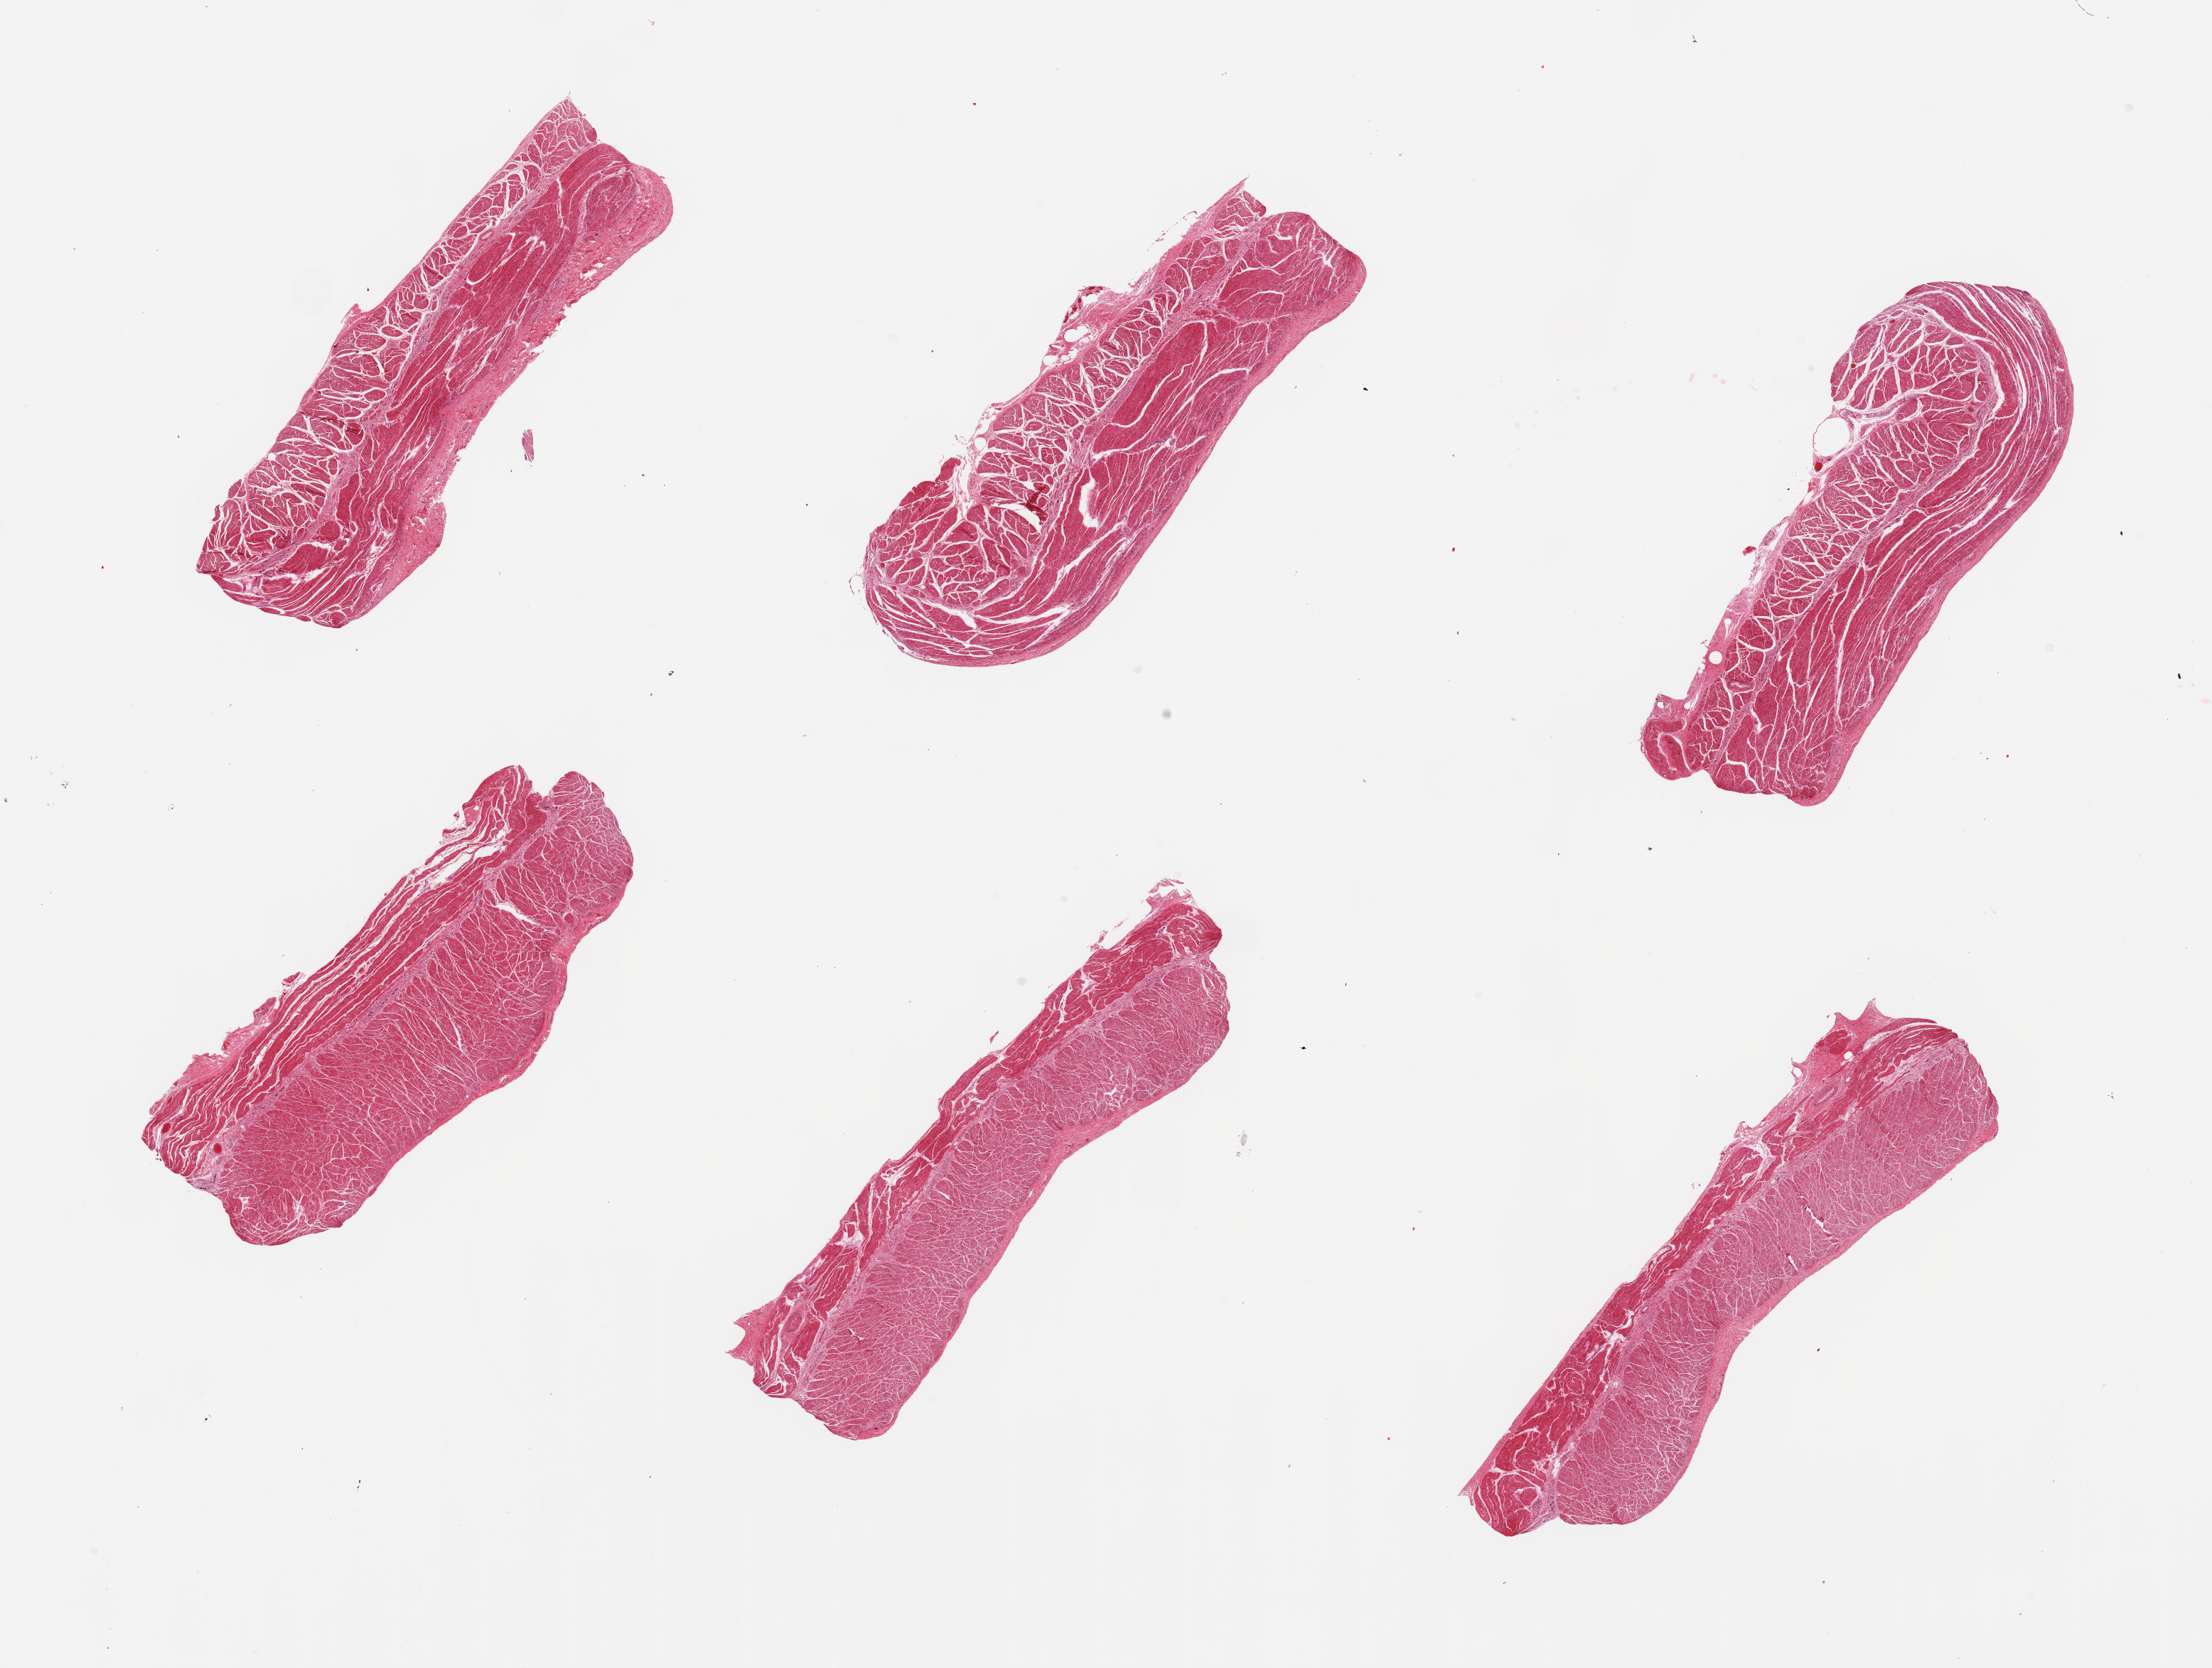
Digitized H&E-stained section — whole scanned area (about 24.6 x 18.6 mm, slide scanned at 20x) shown as a low-resolution overview; PAXgene-fixed paraffin-embedded (PFPE) section; sampled site (target tissue): gastroesophageal junction; donor tissue sample. Donor sex: male.
• review note (as recorded): 6 pieces, confirmed target muscularis